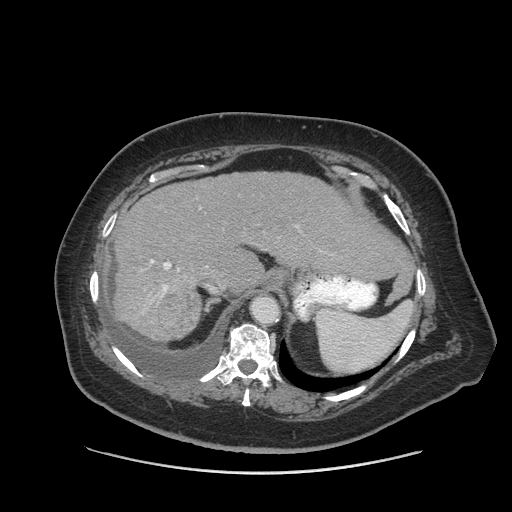
Contrast-enhanced abdominal CT (liver protocol), one axial slice. Position 62 of 91 along the scan axis. Reconstruction kernel STANDARD. 140 kVp. Soft-tissue window (W 400 / L 40 HU). 2.5 mm slice thickness. 512 × 512 image matrix, field of view 420 × 420 mm. Case-level facts recorded for this patient, not image findings: diagnosis: hepatocellular carcinoma (patient treated with transarterial chemoembolisation; whether this scan precedes or follows treatment is not stated here); TNM stage (as recorded): Stage-I; Child-Pugh class: A; tumour differentiation: well differentiated.
Outlined on this slice (semi-automatically segmented with operator editing):
- liver parenchyma outside the tumour (the mass and vessels are separate outlines, so this box may not span the whole liver): bounding box [x1, y1, x2, y2] px = [114, 172, 400, 340]
- mass: [158, 286, 202, 342]
- liver vessels: [151, 260, 179, 297]